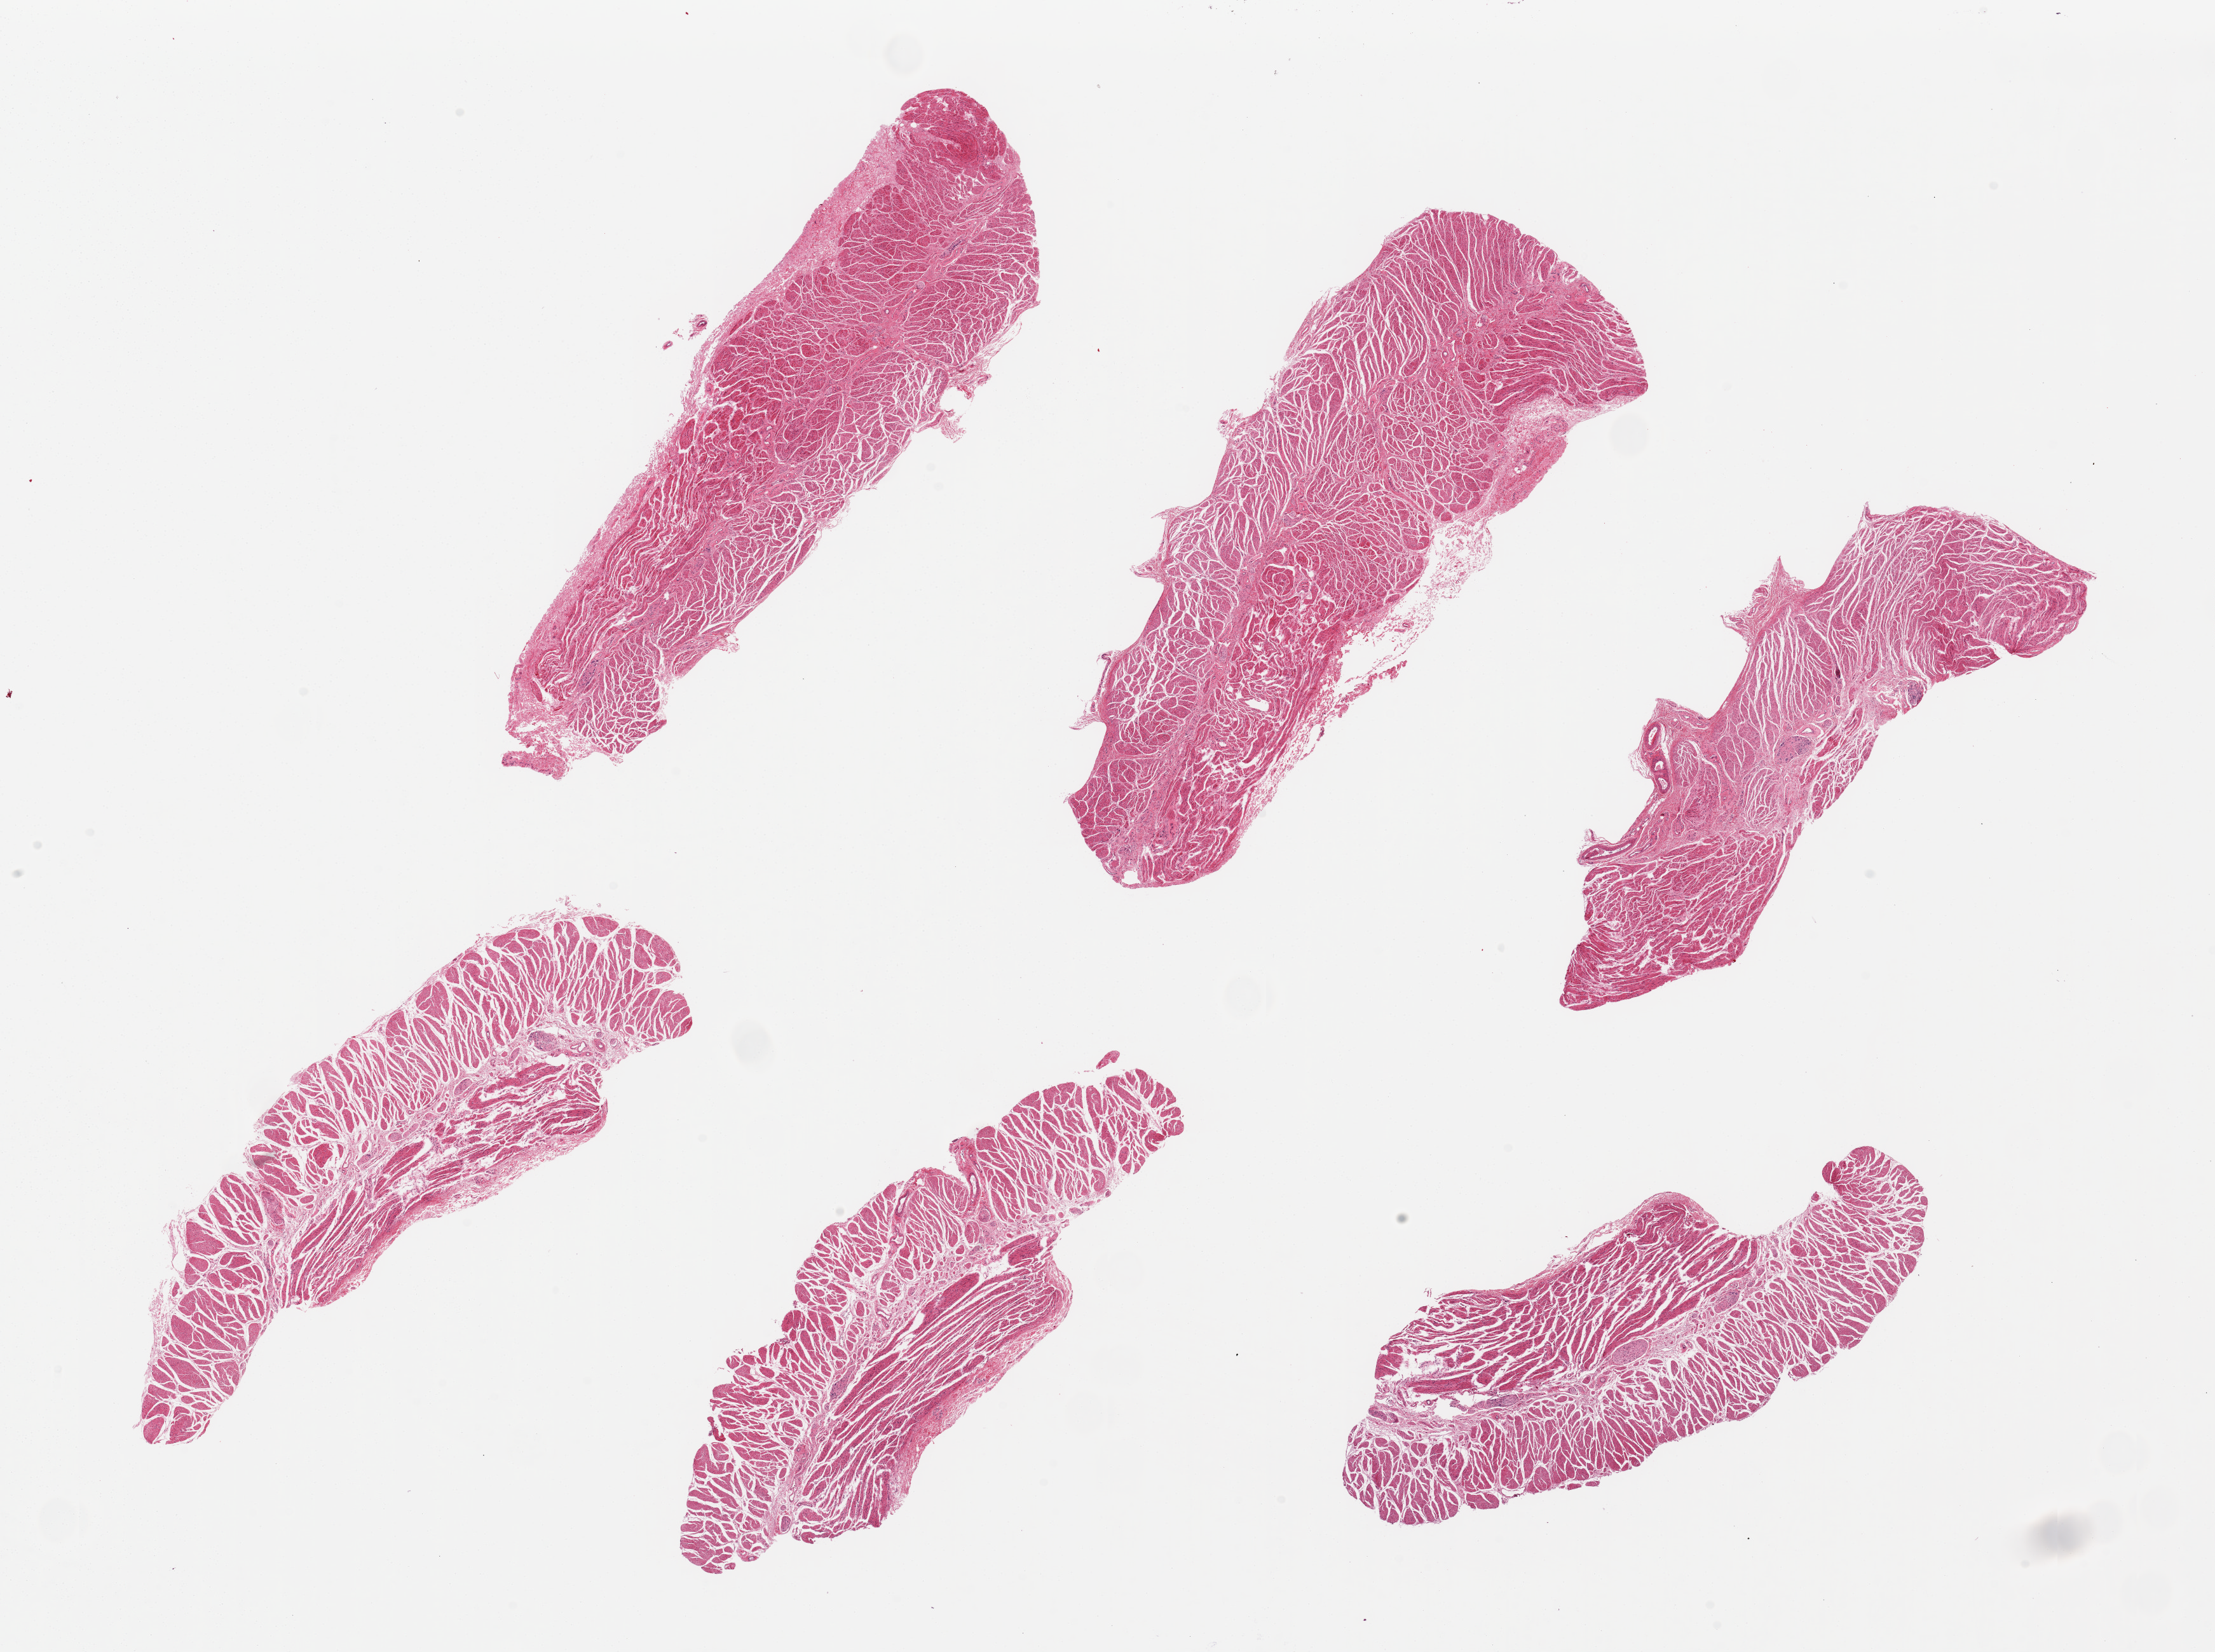
Hematoxylin and eosin (H&E) whole-slide image, low-resolution overview of the scanned area, about 27.6 x 20.6 mm (acquisition: 20x scan); PAXgene-fixed paraffin-embedded (PFPE) section; target tissue: gastroesophageal junction; donor tissue sample. Female donor.
Pathologist's review note for this sample: 6 pieces, up to 10x3.5mm; all muscle as targeted.